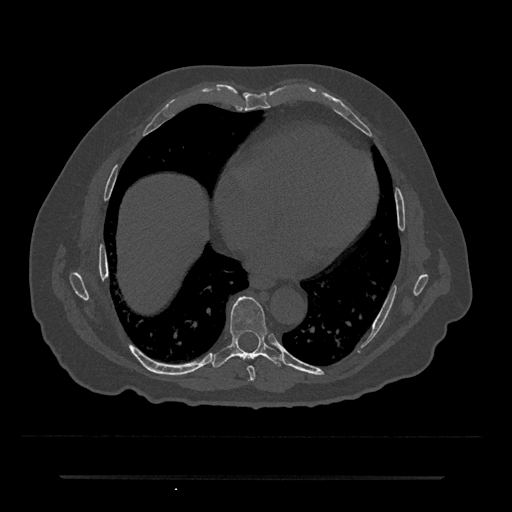
CT including the spine, one axial slice. Position 343 of 797 along the scan axis. Reconstruction kernel Br40s/3. Bone window (W 1800 / L 400 HU). 512 × 512 image matrix, field of view 437 × 437 mm. Patient: male, 69 years. From the clinical record (not read from this slice): primary cancer: prostate.
Structures marked on this image (semi-automatic segmentation, software-assisted and operator-edited):
- T7 vertebra: bounding box (x1, y1, x2, y2) in pixels: (247, 366, 255, 381)
- T8 vertebra: (212, 296, 282, 368)